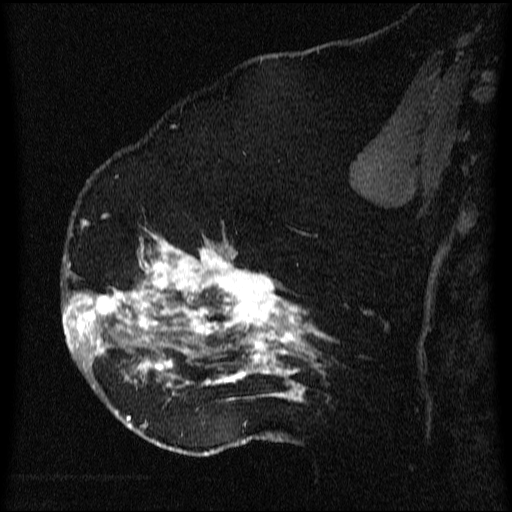
Breast MRI (dynamic contrast-enhanced), one sagittal slice. Position 40 of 64 along the scan axis. Dynamic contrast-enhanced series, image 2 of 3 at this slice position (ordered by acquisition). 1.5 T. TE 4.2 ms, TR 9.1 ms. 2.2 mm slice thickness. 512 × 512 image matrix, field of view 180 × 180 mm. Patient: female, 52 years.
Outlined on this slice (semi-automatically segmented with operator editing):
- analysis volume of interest (the breast-tissue region the enhancement analysis was run in; not a lesion): bounding box [x1, y1, x2, y2] px = [61, 203, 348, 438]
- tumour enhancement mask (voxels above the 70 % enhancement threshold inside the analysis volume of interest): [63, 224, 331, 438]